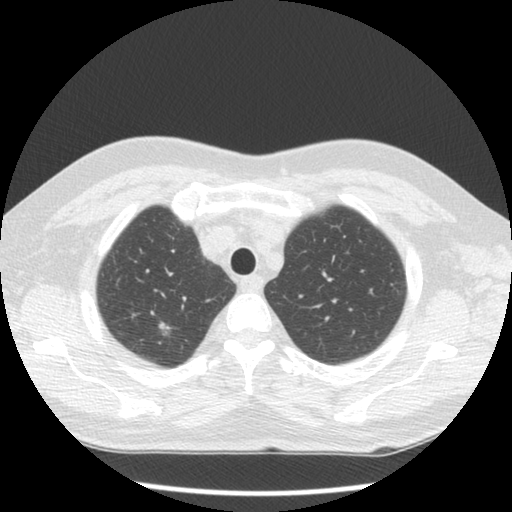
Low-dose screening chest CT, one axial slice; 120 kVp; lung window (W 1500 / L -600 HU); 2.5 mm slice thickness; 512 × 512 image matrix, field of view 332 × 332 mm.
Structures marked on this image (outlined manually by an expert reader):
- lesion 1 (tumor, upper lobe of right lung): bounding box [x1, y1, x2, y2] px = [159, 322, 172, 336]